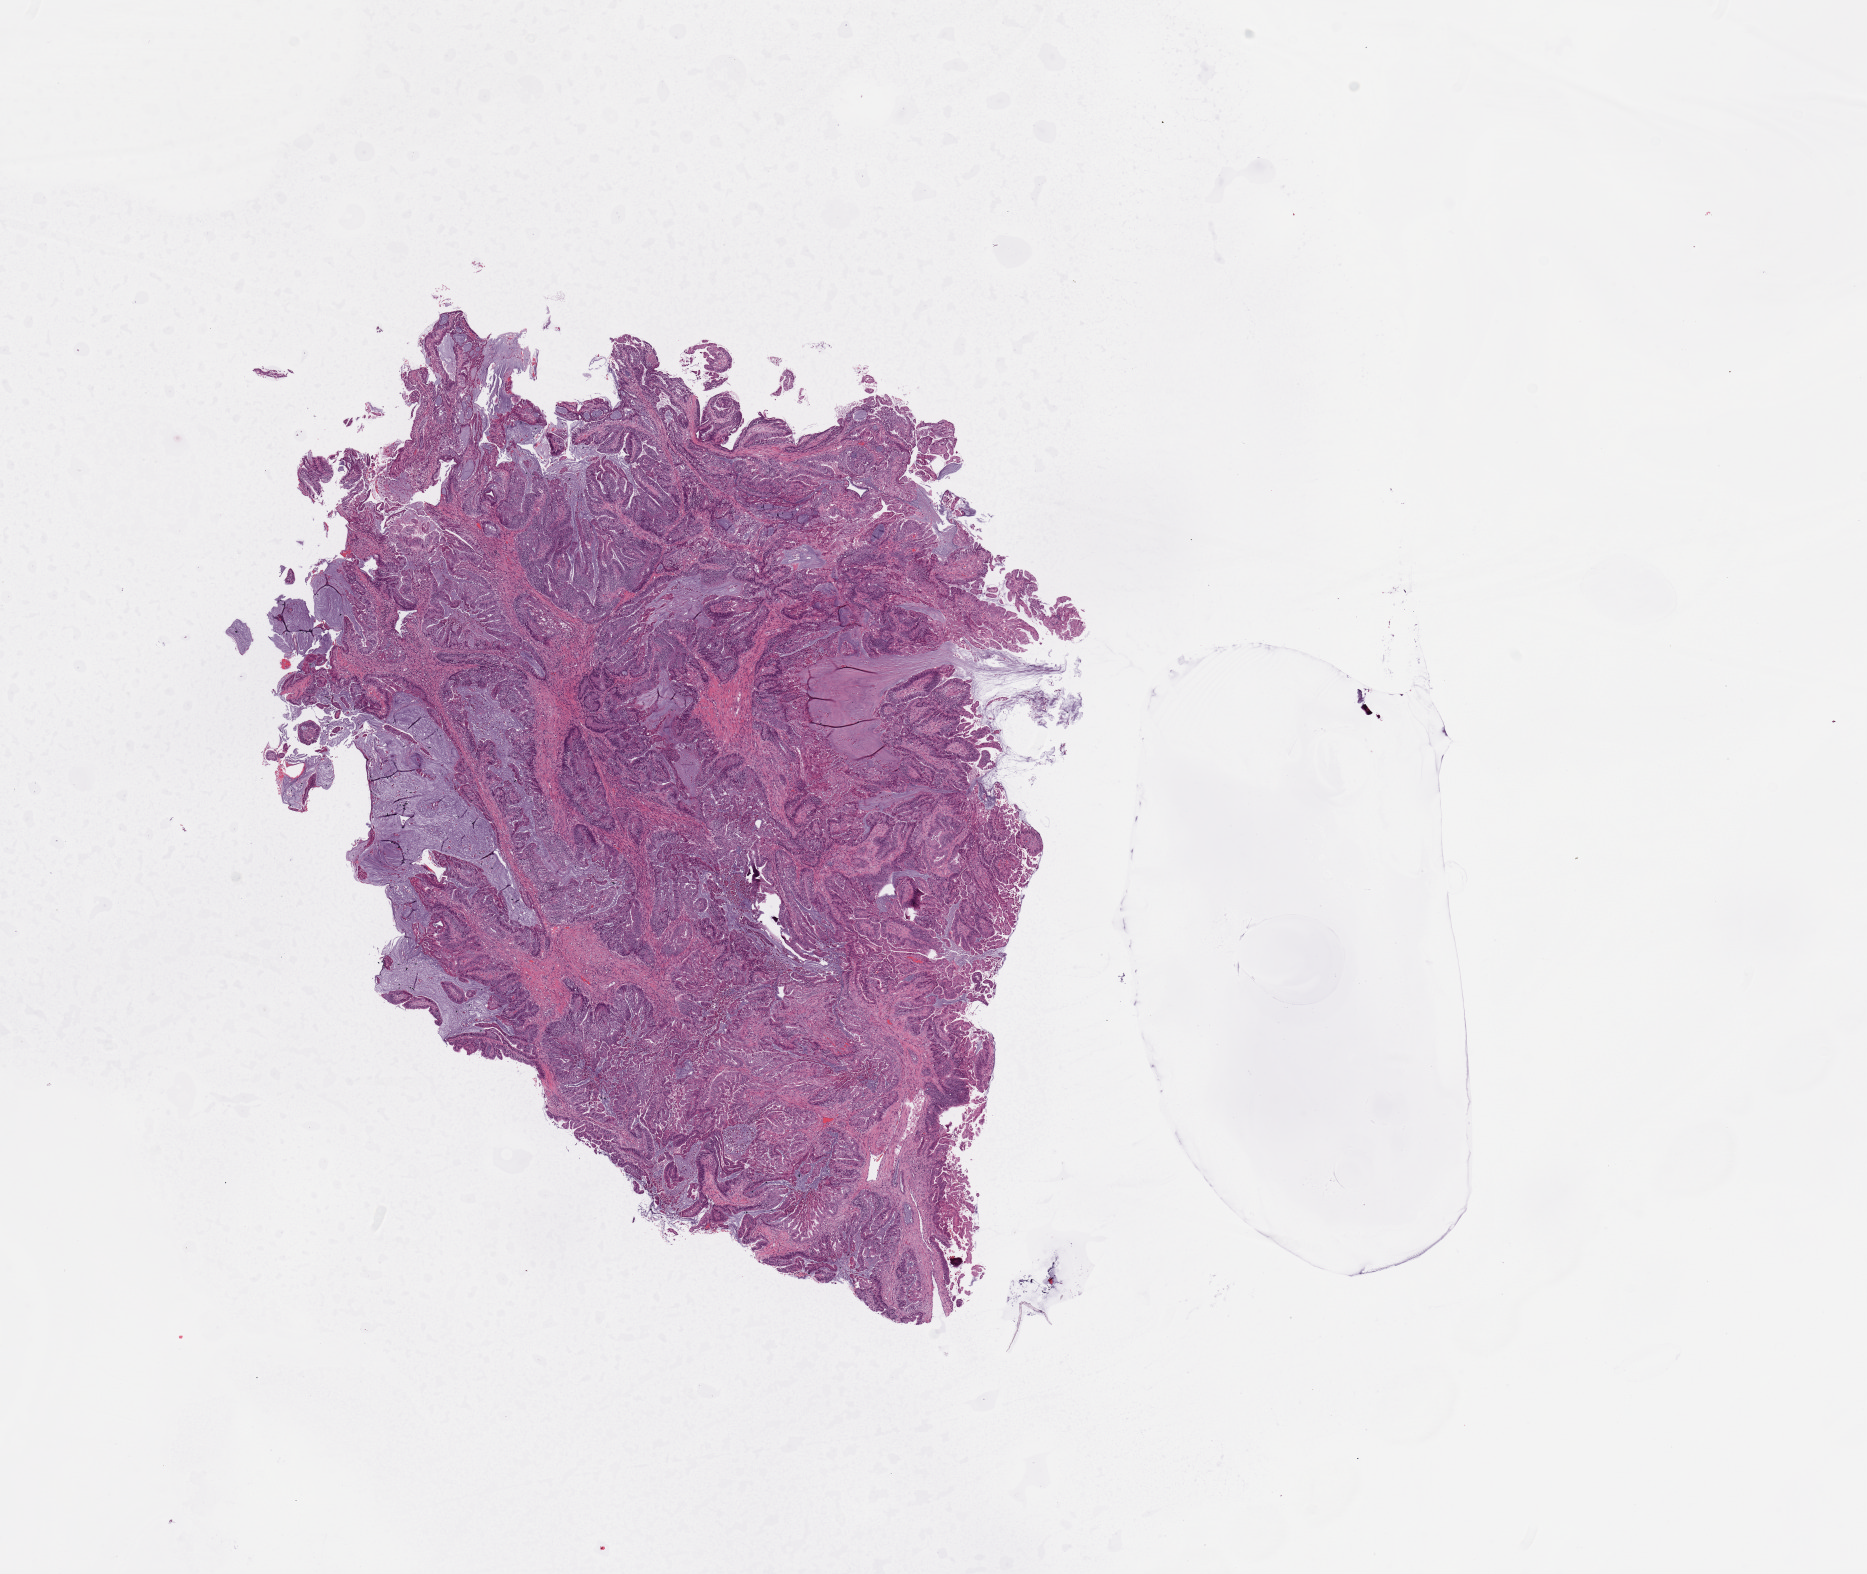
Digitized Hematoxylin and eosin (H&E) stained tissue section (whole slide) — whole scanned area (about 14.8 x 12.4 mm) shown as a low-resolution overview. Tumour tissue sample, sampled site: uterus. Patient: female, age 46 years. Histologic grade: G2 (moderately differentiated). Slide review estimates, as recorded: tumour nuclei 80%, necrosis 0%.
AJCC pathologic stage: I. Histologic diagnosis: Endometrioid adenocarcinoma, NOS.